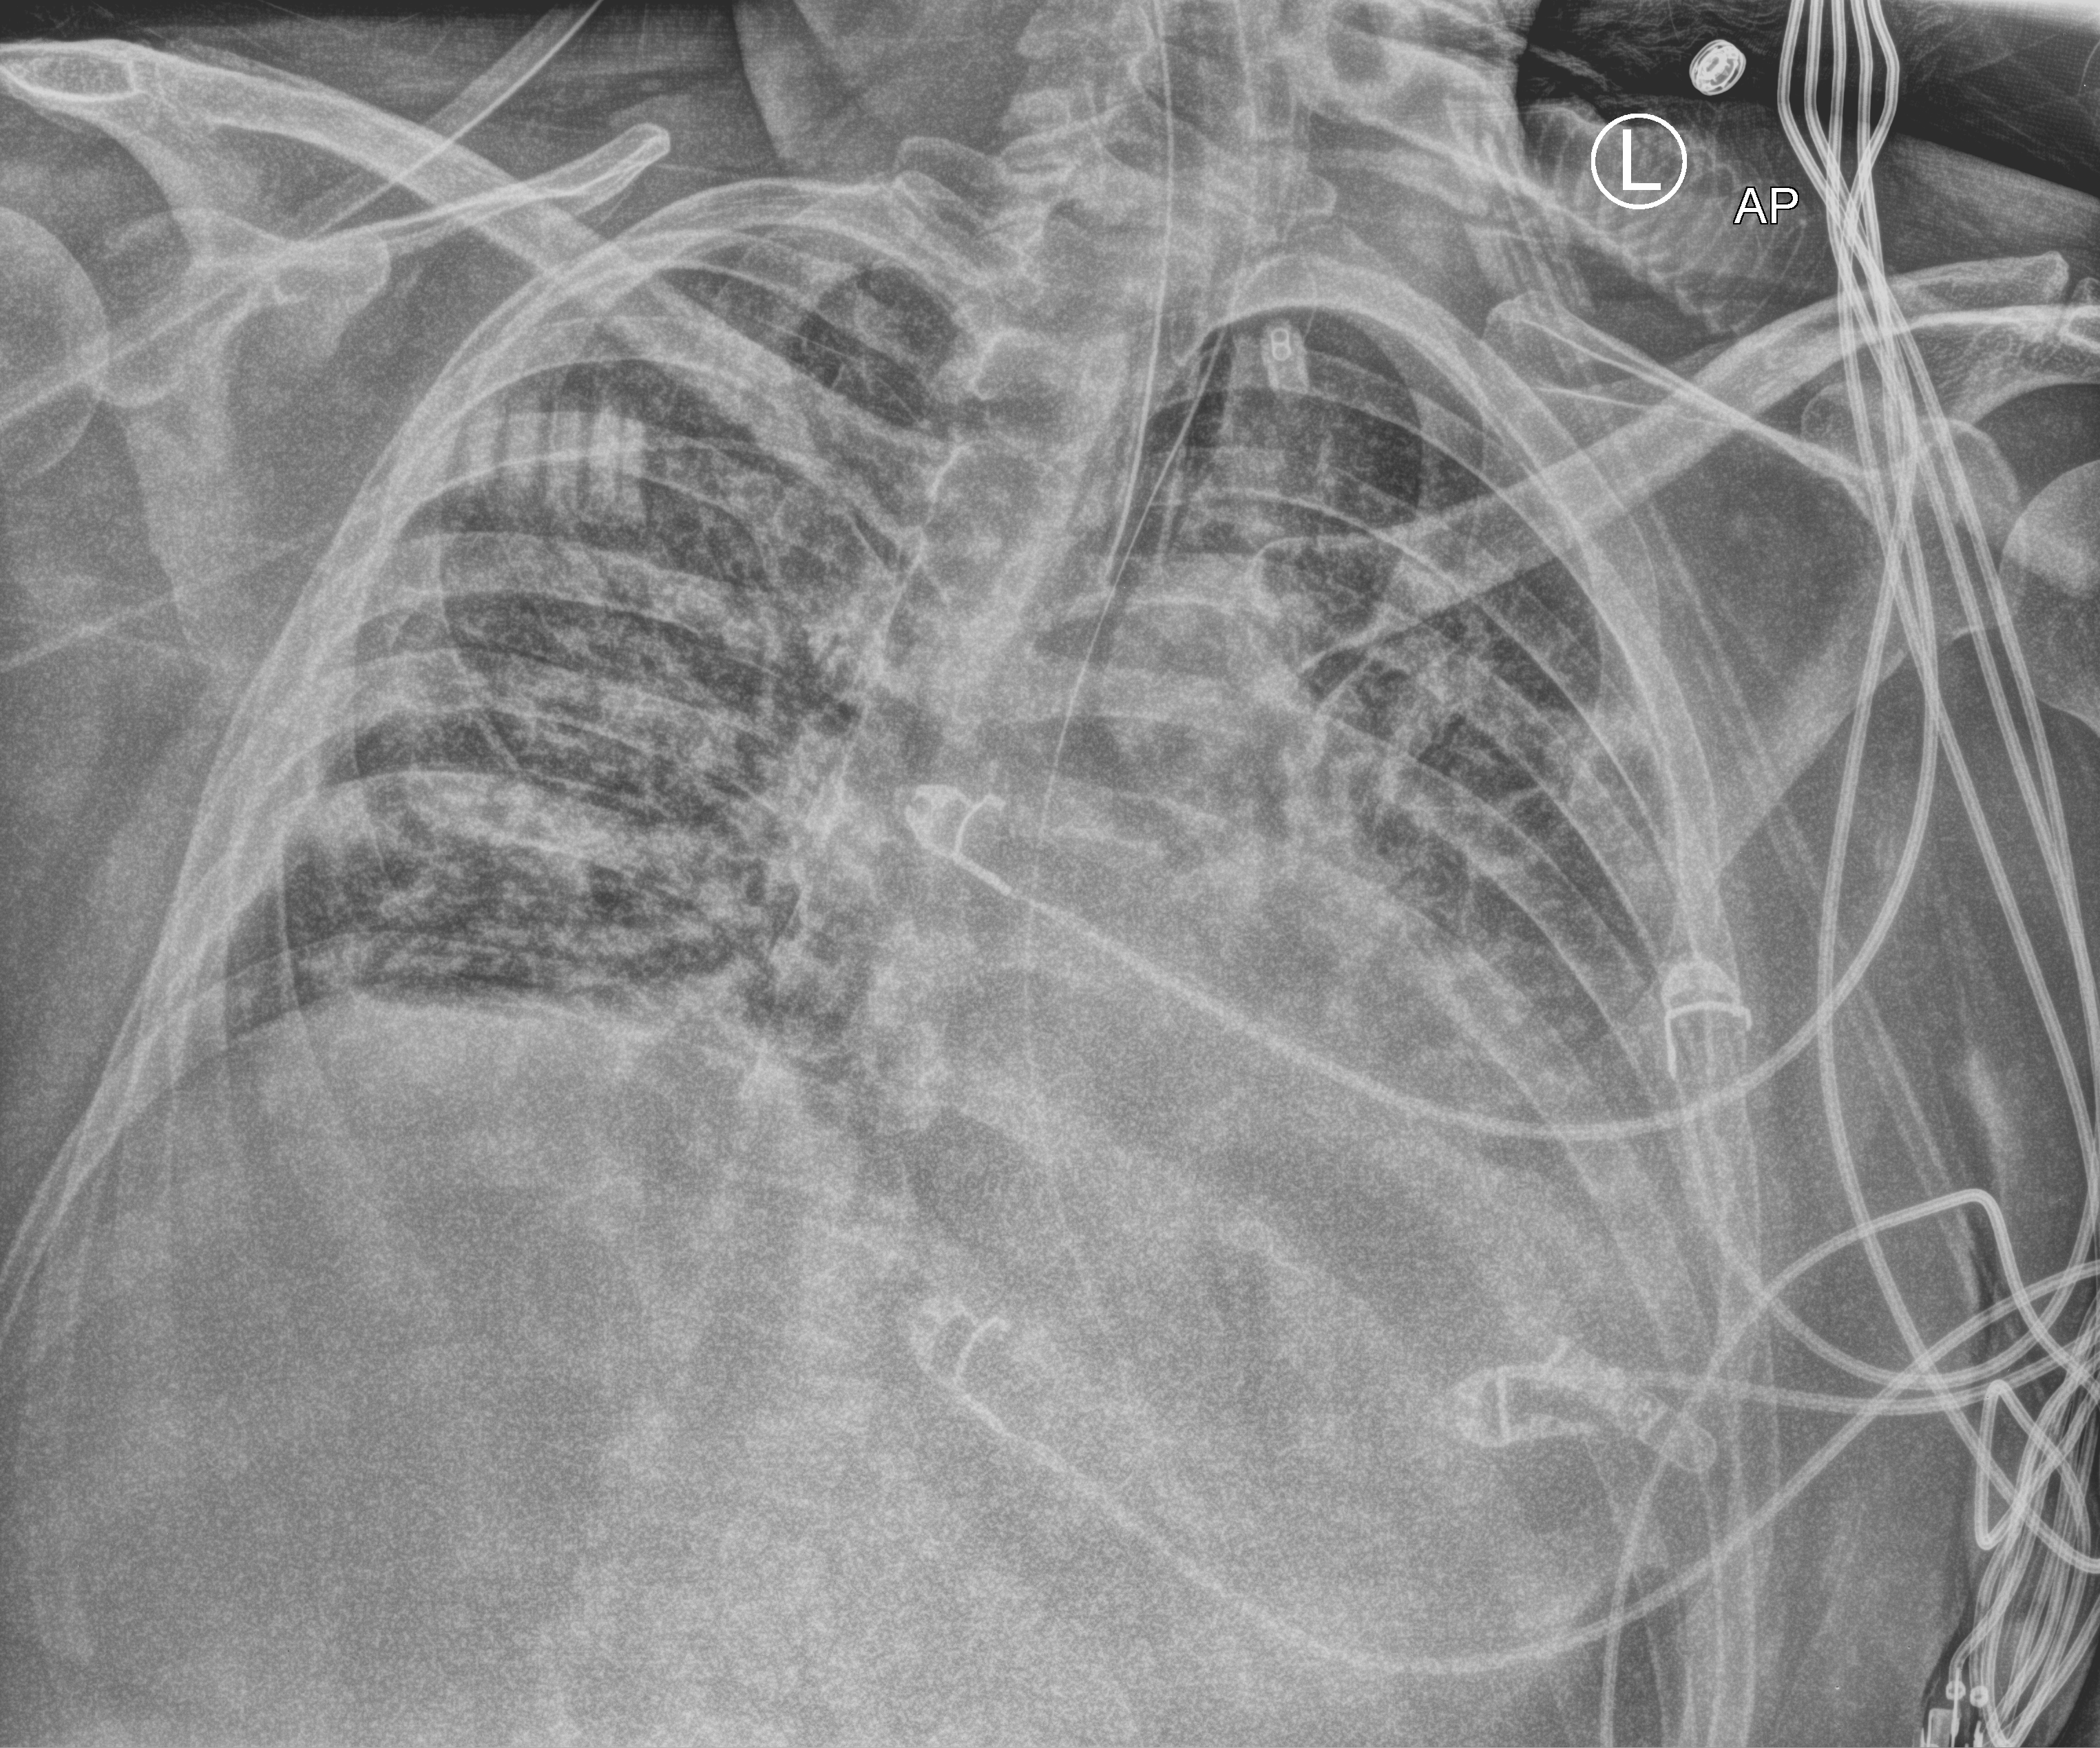
Chest X-ray (portable); anteroposterior (AP) projection. Patient hospitalised with COVID-19; male, aged 18–59 years.
Hospital-stay facts (about this admission, not read from this image; timing relative to this image not recorded): hypertension (admission record): yes; mechanically ventilated during this hospital stay: yes.